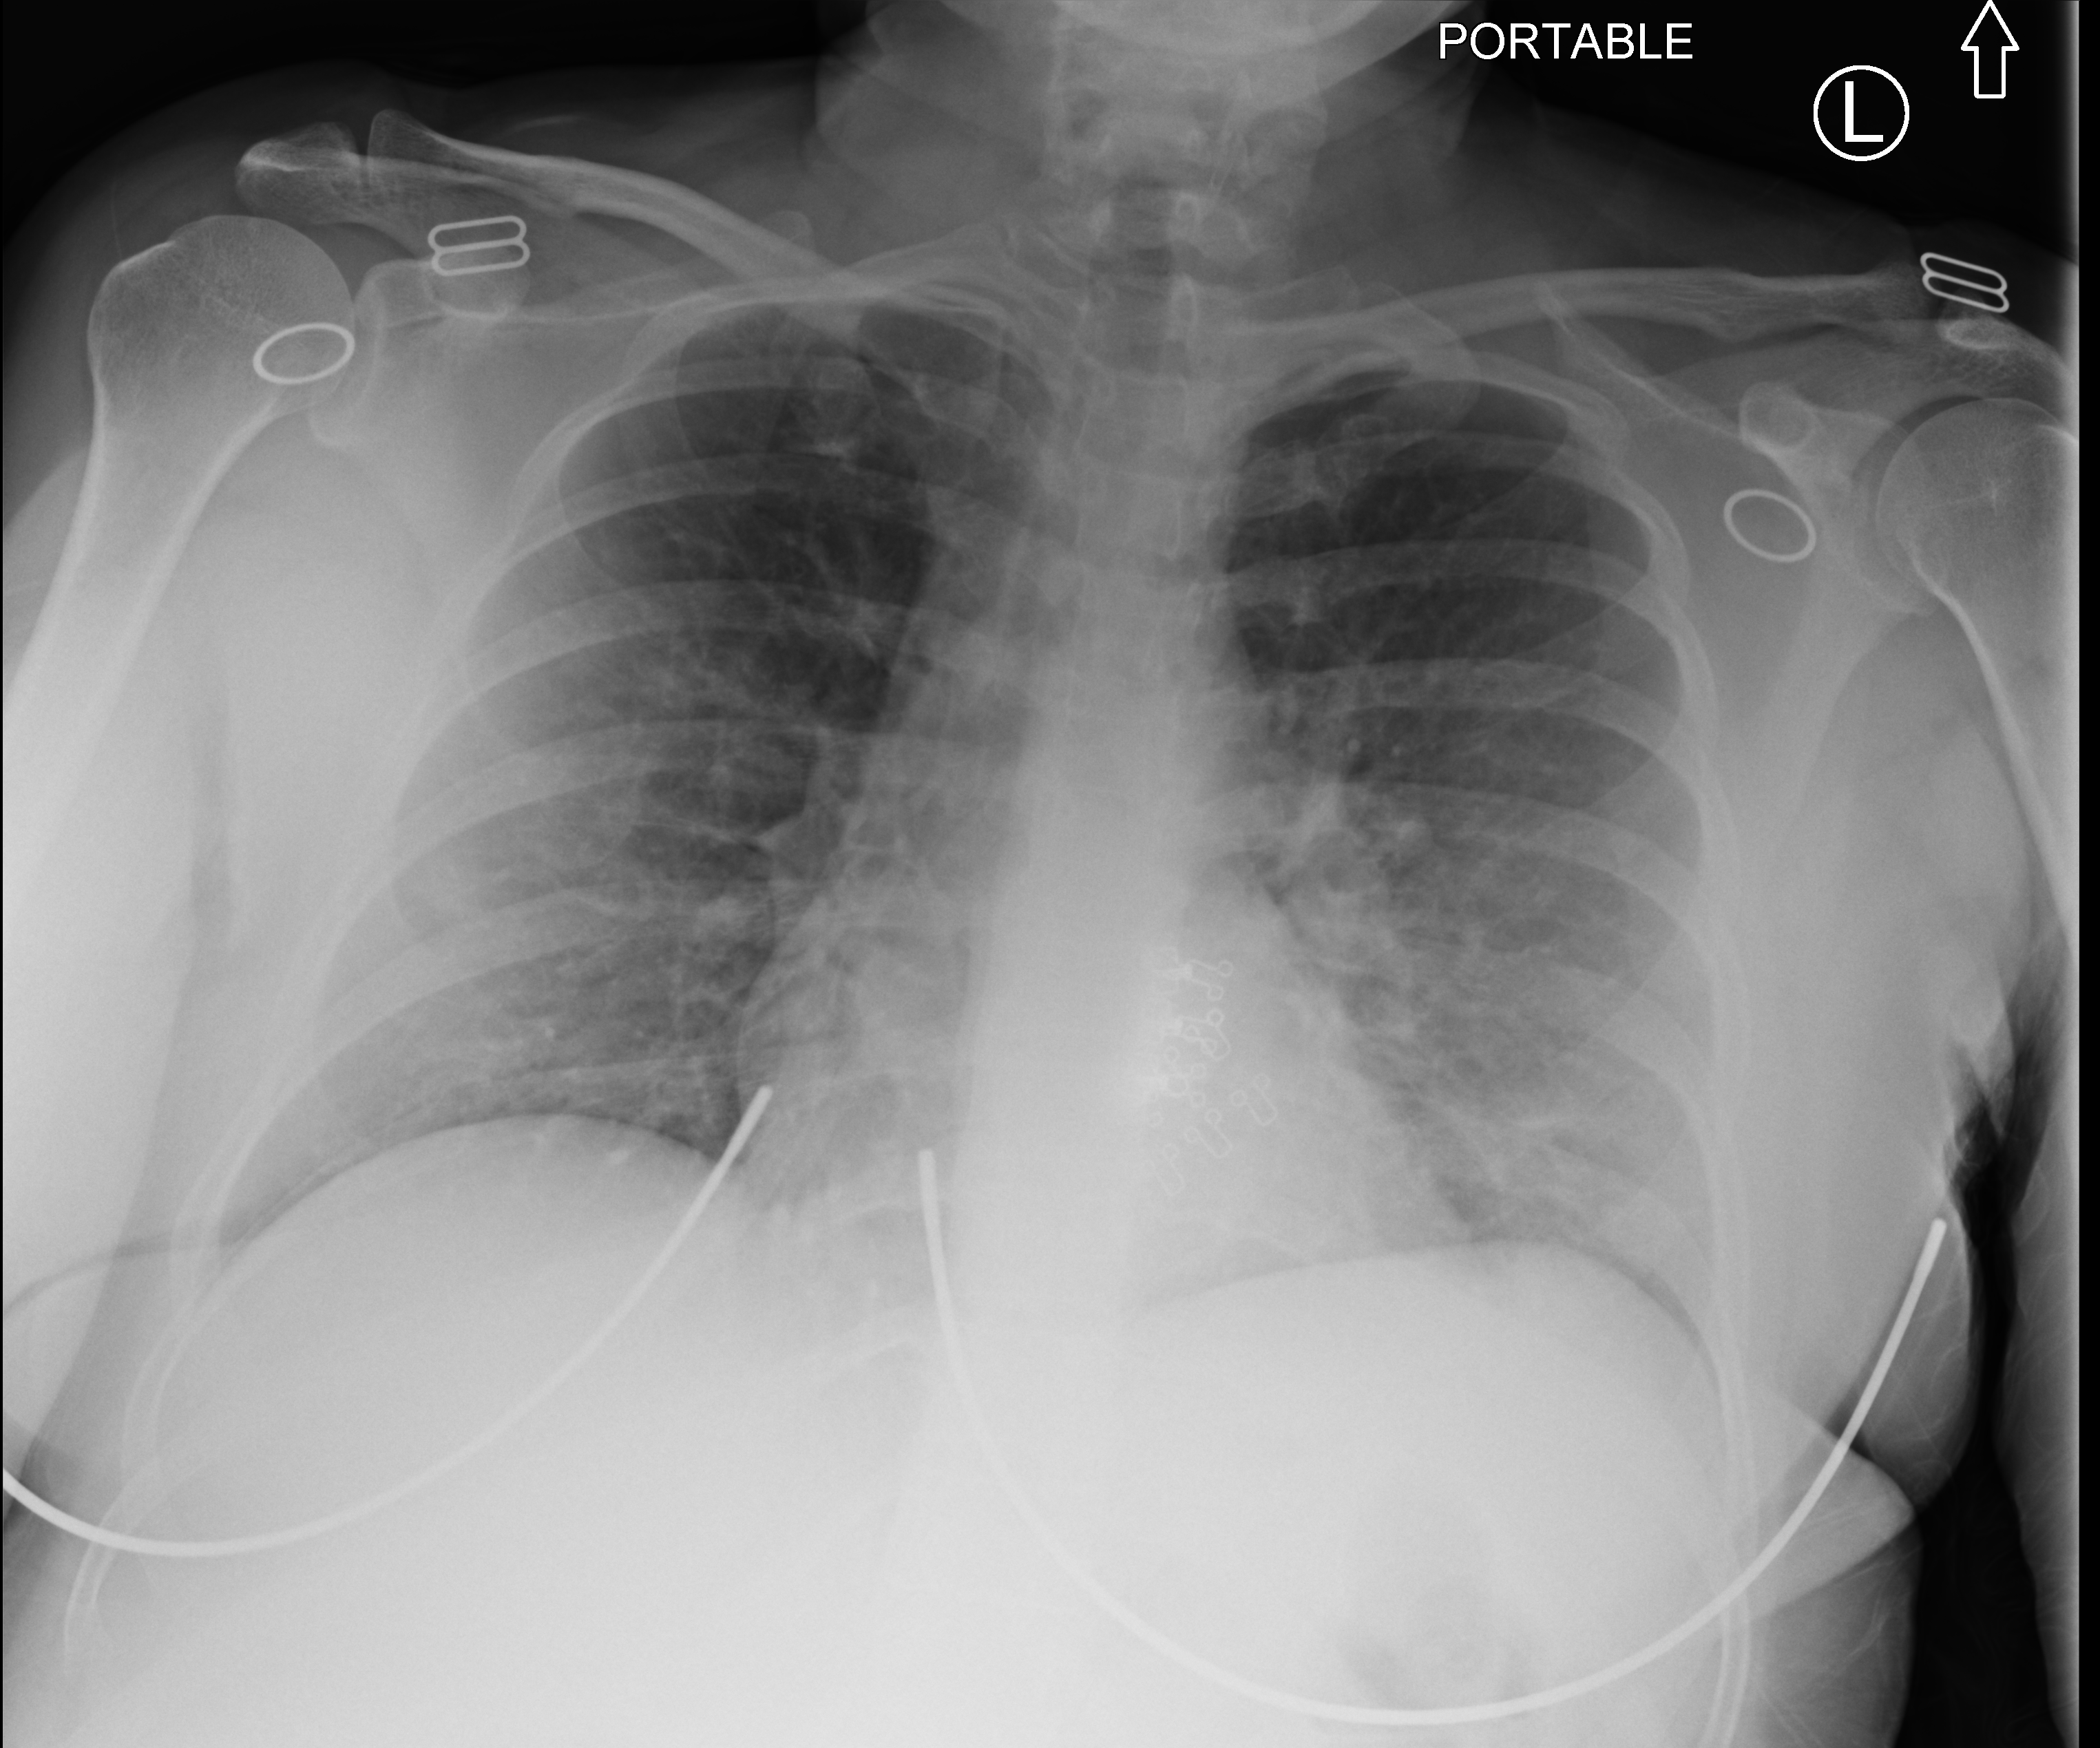
Portable chest radiograph, anteroposterior (AP) projection. Female patient hospitalised with COVID-19, age 18–59 years.
Hospital-stay facts (about this admission, not read from this image; timing relative to this image not recorded): admitted to intensive care during this hospital stay: no; mechanically ventilated during this hospital stay: no.